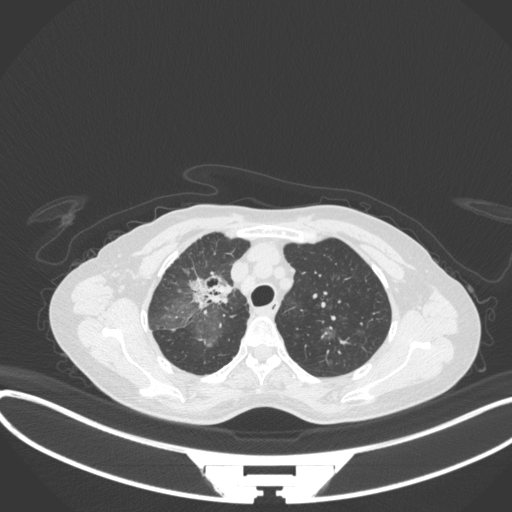
Chest CT, one axial slice. Slice 246 of 311 in the series (ordered by position). Reconstruction kernel B31f. 120 kVp. Lung window (W 1500 / L -600 HU). 1 mm slice thickness. 512 × 512 image matrix. Patient: female, 59 years. From the clinical record (not read from this slice): clinical TNM (as recorded): T3 N0 M0; histopathological grade: G1.
Annotated regions visible in this slice (rectangle marked by the reading radiologist):
- lung tumour (recorded histology: adenocarcinoma): box from (x=187, y=265) to (x=235, y=313) px